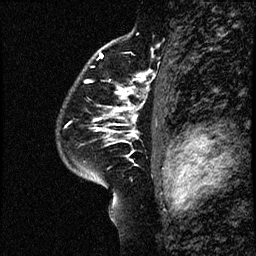
Breast MRI (dynamic contrast-enhanced), one sagittal slice. Slice 43 of 60 in the series (ordered by position). Dynamic contrast-enhanced study with each time point stored as its own series, time point 2 of 4 at this slice position (early post-contrast, ordered by acquisition time). 1.5 T. TE 4.2 ms, TR 17.6 ms. 256 × 256 image matrix. Female patient, age 43 years. From the clinical record (not read from this slice): setting: breast cancer imaged before/during neoadjuvant chemotherapy.
Outlined on this slice (semi-automatic segmentation, software-assisted and operator-edited):
- analysis volume of interest (the breast-tissue region the enhancement analysis was run in; not a lesion): box from (x=60, y=95) to (x=169, y=191) px
- tumour enhancement mask (voxels above the 100 % enhancement threshold inside the analysis volume of interest): (x=98, y=95)–(x=136, y=137)